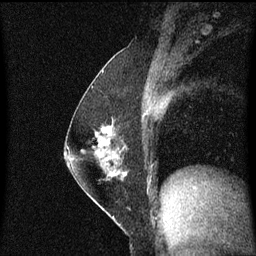
Breast MRI (dynamic contrast-enhanced), one sagittal slice. Position 31 of 60 along the scan axis. Dynamic contrast-enhanced series, image 2 of 3 at this slice position (ordered by acquisition). 1.5 T. TE 4.2 ms, TR 8.4 ms. 2 mm slice thickness. 256 × 256 image matrix. Patient: female, 52 years. Case-level facts recorded for this patient, not image findings: setting: breast cancer imaged before/during neoadjuvant chemotherapy; receptor status: HER2-positive.
Outlined on this slice (semi-automatic segmentation, software-assisted and operator-edited):
- analysis volume of interest (the breast-tissue region the enhancement analysis was run in; not a lesion): bounding box <71,118,130,187> (left, top, right, bottom; pixels)
- tumour enhancement mask (voxels above the 70 % enhancement threshold inside the analysis volume of interest): <98,126,112,141>